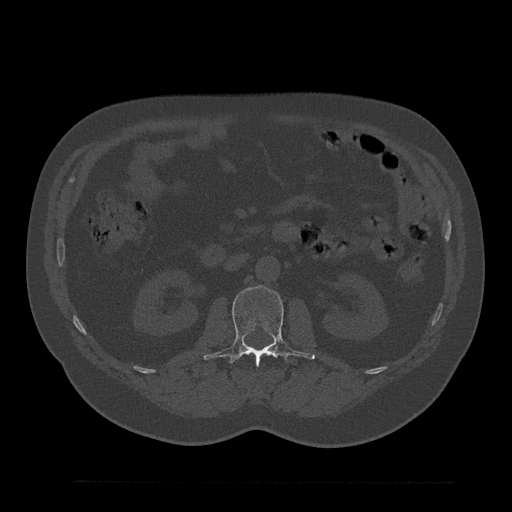
CT including the spine, one axial slice. Slice 105 of 797 in the series (ordered by position). Bone window (W 1800 / L 400 HU). 0.5 mm slice thickness. 512 × 512 image matrix, field of view 430 × 430 mm. Patient: male, 61 years. From the clinical record (not read from this slice): primary cancer: prostate.
Annotated regions visible in this slice (semi-automatically segmented with operator editing):
- L1 vertebra: box from (x=263, y=353) to (x=272, y=356) px
- L2 vertebra: (x=204, y=286)–(x=315, y=364)